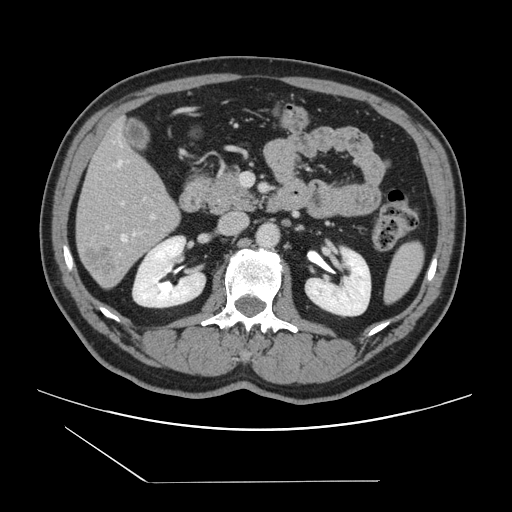
Contrast-enhanced abdominal CT, one axial slice. Position 61 of 157 along the scan axis. 120 kVp. Intravenous contrast given. Soft-tissue window (W 400 / L 40 HU). 2.5 mm slice thickness. 512 × 512 image matrix, field of view 407 × 407 mm. Male patient, age 61 years. Case-level facts recorded for this patient, not image findings: diagnosis: colorectal cancer liver metastases, imaged before liver resection; multiple liver metastases: yes; largest metastasis: 5.5 cm; disease in both lobes: yes.
Structures marked on this image (expert manual segmentation):
- hepatic veins: bounding box <118,160,136,241> (left, top, right, bottom; pixels)
- liver: <76,123,180,288>
- planned liver remnant (the part of the liver to remain after resection): <78,123,171,218>
- portal vein (with intrahepatic branches): <106,201,155,228>
- liver metastasis: <82,243,118,284>